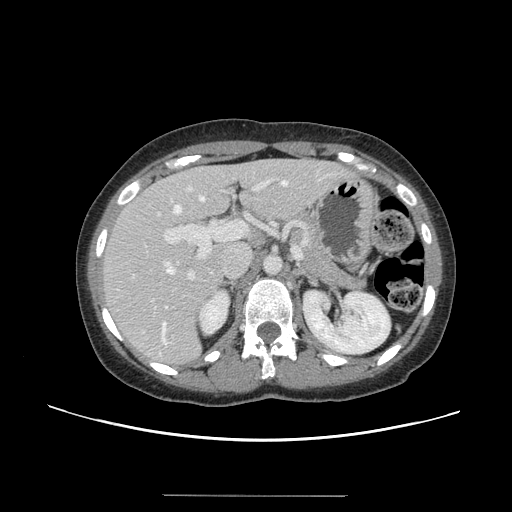
Contrast-enhanced abdominal CT, one axial slice; position 86 of 144 along the scan axis; 120 kVp; soft-tissue window (W 400 / L 40 HU); 2.5 mm slice thickness; 512 × 512 image matrix. Female patient, age 53 years. Case-level facts recorded for this patient, not image findings: diagnosis: colorectal cancer liver metastases, imaged before liver resection; multiple liver metastases: yes; largest metastasis: 1.1 cm.
Structures marked on this image (manually delineated by an expert):
- hepatic veins: bounding box (x1, y1, x2, y2) in pixels: (163, 180, 287, 343)
- liver: (104, 160, 350, 364)
- planned liver remnant (the part of the liver to remain after resection): (105, 159, 315, 297)
- portal vein (with intrahepatic branches): (133, 179, 301, 302)